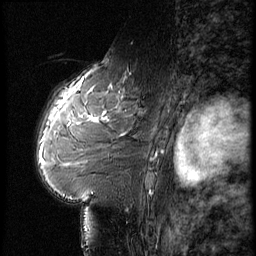
Breast MRI (dynamic contrast-enhanced), one sagittal slice; dynamic contrast-enhanced series, image 2 of 3 at this slice position (ordered by acquisition); 1.5 T; TE 4.2 ms, TR 9 ms; 2.5 mm slice thickness; 256 × 256 image matrix, field of view 180 × 180 mm. Female patient, age 61 years. From the clinical record (not read from this slice): setting: breast cancer imaged before/during neoadjuvant chemotherapy; receptor status: HR-positive, HER2-negative.
Annotated regions visible in this slice (semi-automatically segmented with operator editing):
- analysis volume of interest (the breast-tissue region the enhancement analysis was run in; not a lesion): bounding box (x1, y1, x2, y2) in pixels: (65, 74, 149, 175)
- tumour enhancement mask (voxels above the 140 % enhancement threshold inside the analysis volume of interest): (90, 115, 99, 120)